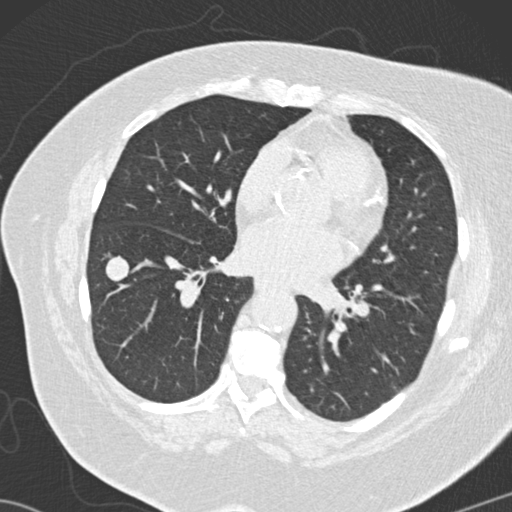
Low-dose screening chest CT, one axial slice. Position 63 of 146 along the scan axis. Reconstruction kernel B30f. 120 kVp. Lung window (W 1500 / L -600 HU). 2 mm slice thickness. 512 × 512 image matrix.
Annotated regions visible in this slice (expert manual segmentation):
- lesion 2 (tumor, lower lobe of right lung): bounding box (x1, y1, x2, y2) in pixels: (105, 256, 130, 282)